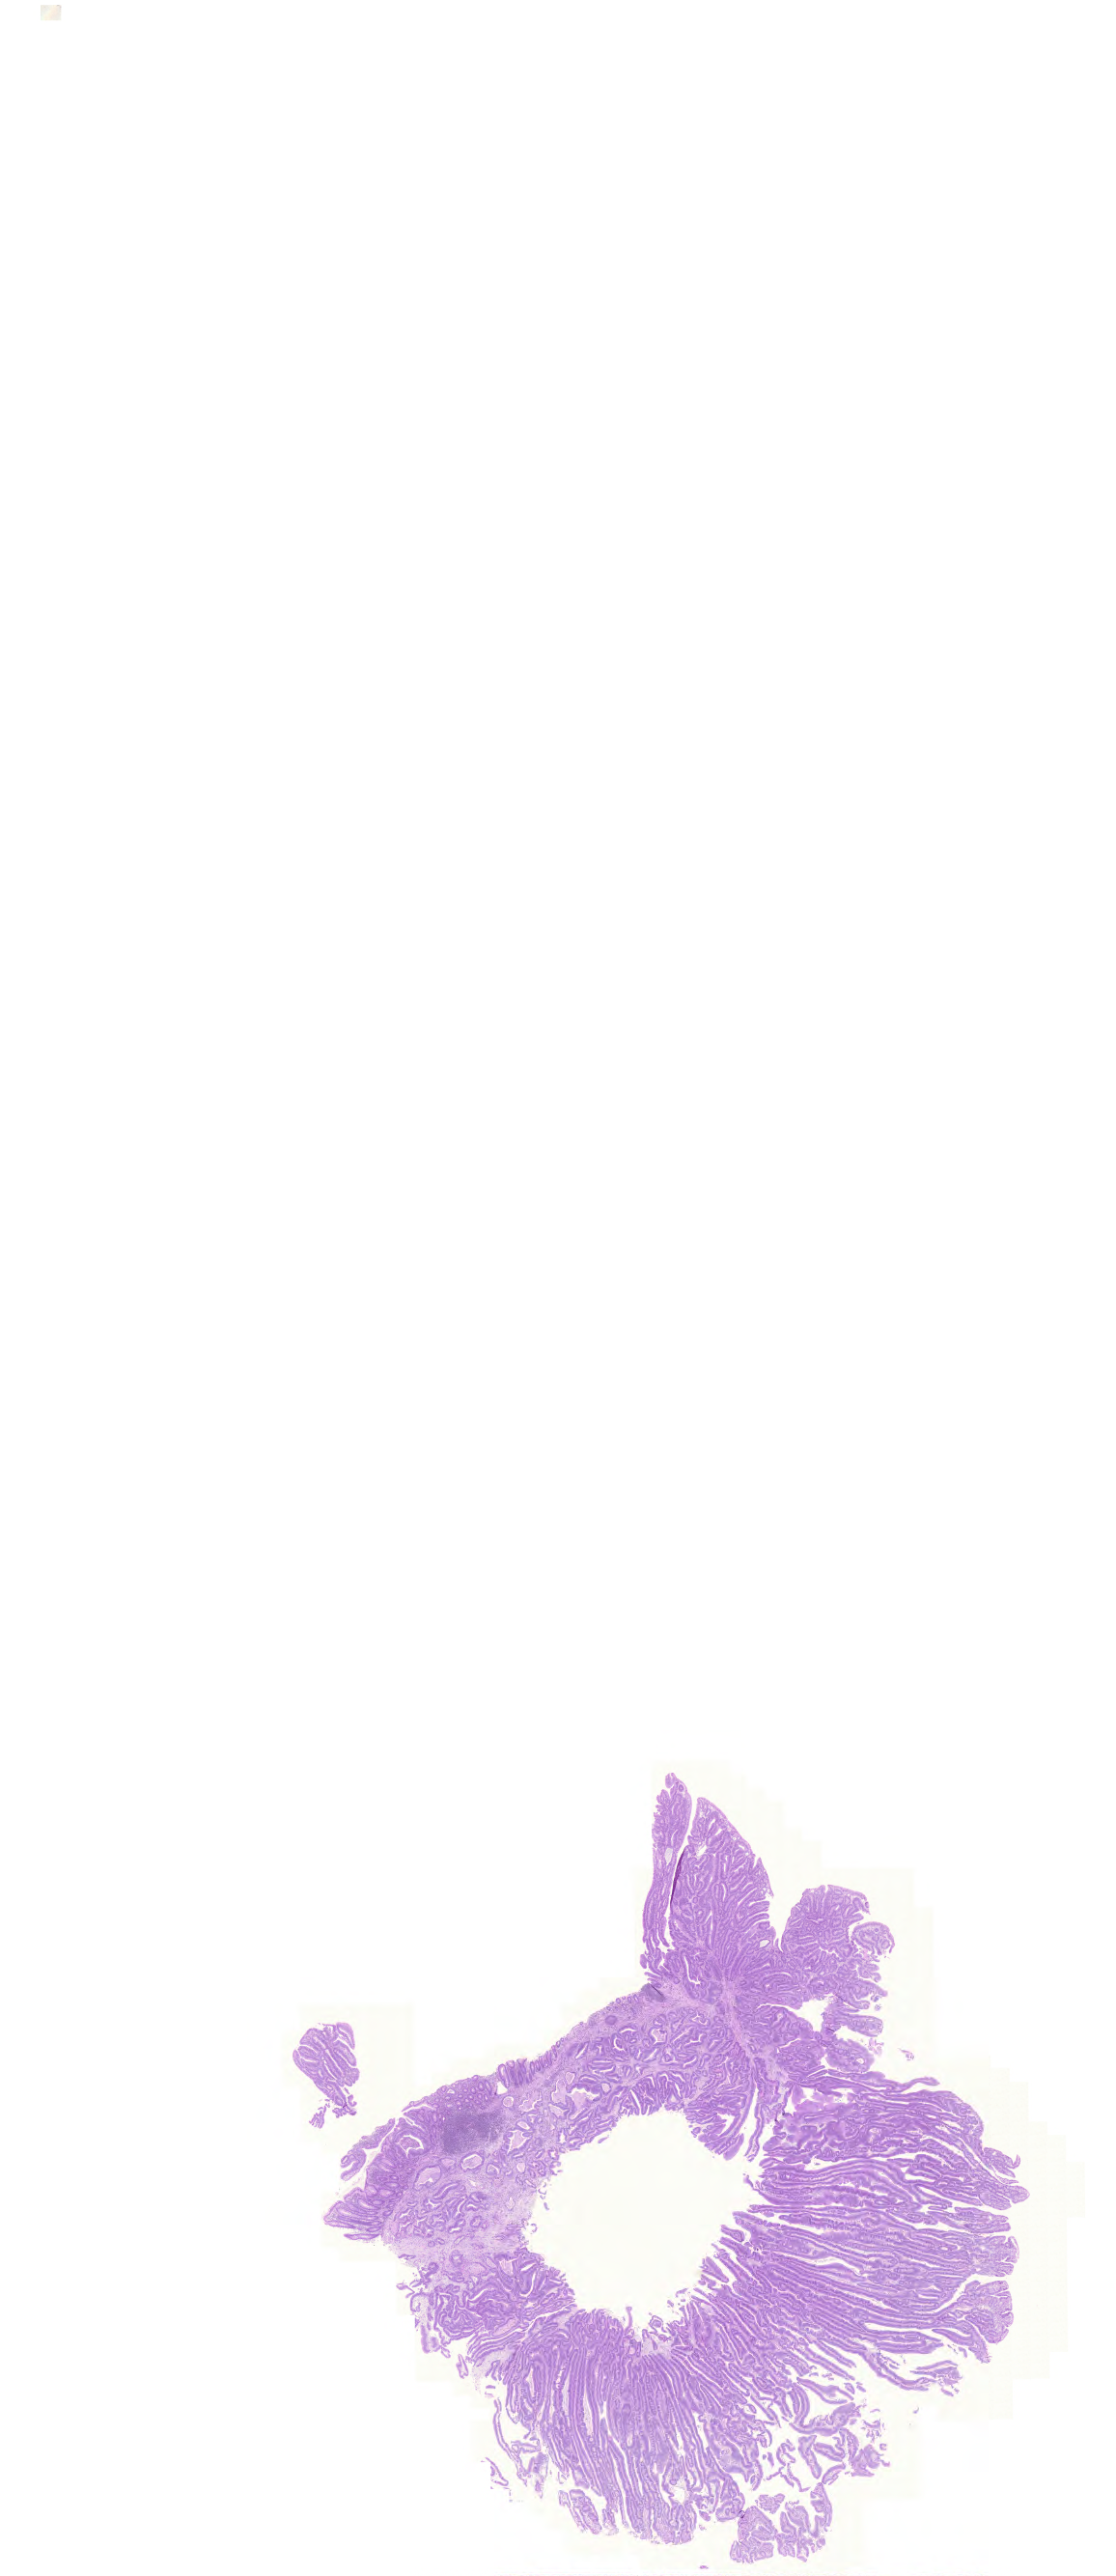
Whole-slide histology image, Hematoxylin and eosin (H&E) stained — low-resolution overview of the scanned area, about 17.2 x 39.7 mm. Formalin-fixed paraffin-embedded (FFPE) diagnostic section. Sample: primary tumour, colon. Patient: male, age at initial diagnosis 68 years.
AJCC pathologic stage: III (5th edition). Lymph nodes positive (case pathology): 2 of 41 examined. Histologic diagnosis: Adenocarcinoma, NOS.